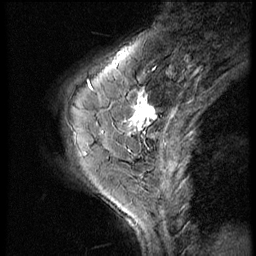
Breast MRI (dynamic contrast-enhanced), one sagittal slice; position 18 of 56 along the scan axis; 3 images stored at this slice position (order not interpretable as contrast timing); 1.5 T; TE 4.2 ms, TR 9 ms; 2.5 mm slice thickness; 256 × 256 image matrix, field of view 180 × 180 mm. Female patient, age 46 years. From the clinical record (not read from this slice): setting: breast cancer imaged before/during neoadjuvant chemotherapy; receptor status: HER2-positive.
Annotated regions visible in this slice (semi-automatically segmented with operator editing):
- analysis volume of interest (the breast-tissue region the enhancement analysis was run in; not a lesion): box from (x=73, y=86) to (x=164, y=161) px
- tumour enhancement mask (voxels above the 140 % enhancement threshold inside the analysis volume of interest): (x=131, y=98)–(x=156, y=130)